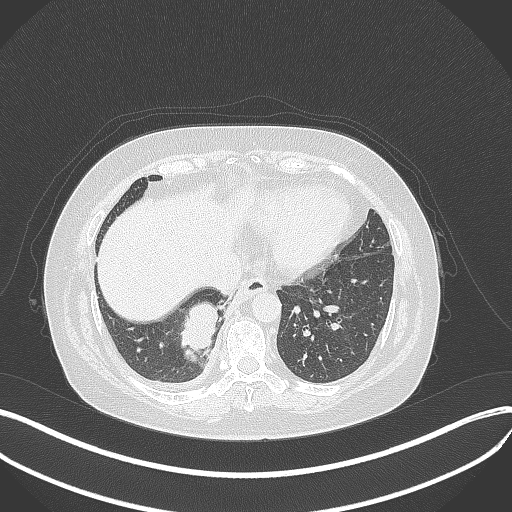
Chest CT, one axial slice. Position 103 of 381 along the scan axis. 120 kVp. Lung window (W 1500 / L -600 HU). 512 × 512 image matrix, field of view 400 × 400 mm. Female patient, age 56 years. Case-level facts recorded for this patient, not image findings: clinical TNM (as recorded): T2b N1 M0.
Outlined on this slice (bounding box drawn by a radiologist):
- lung tumour (recorded histology: small cell carcinoma): bounding box <178,295,227,357> (left, top, right, bottom; pixels)